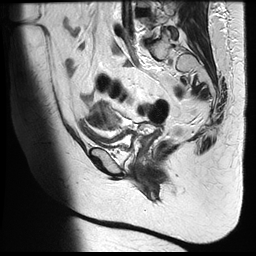
Pelvic MRI for cervical cancer, one sagittal slice. Slice 21 of 35 in the series (ordered by position). T2-weighted. 1.5 T. TE 122.8 ms, TR 4992 ms. 4 mm slice thickness. 256 × 256 image matrix, field of view 300 × 300 mm. Patient: female, 42 years.
Outlined on this slice (expert manual segmentation):
- uterus and cervix: bounding box <88,101,119,130> (left, top, right, bottom; pixels)